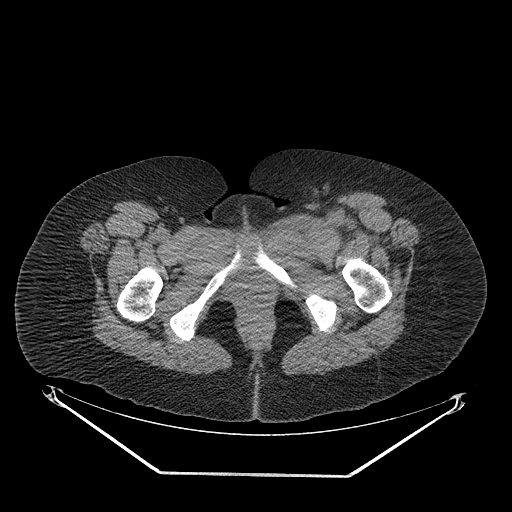
CT of an extremity soft-tissue mass (from a PET/CT study), one axial slice. Slice 48 of 267 in the series (ordered by position). 140 kVp. Soft-tissue window (W 400 / L 40 HU). 3.75 mm slice thickness. 512 × 512 image matrix, field of view 500 × 500 mm. Female patient. Case-level facts recorded for this patient, not image findings: histological type: myxofibrosarcoma; grade: intermediate; site of the primary tumour: left thigh.
Structures marked on this image (expert contour drawn on MRI and transferred to this co-registered scan by the dataset authors):
- gross tumour volume including surrounding oedema: bounding box [x1, y1, x2, y2] px = [265, 208, 362, 250]